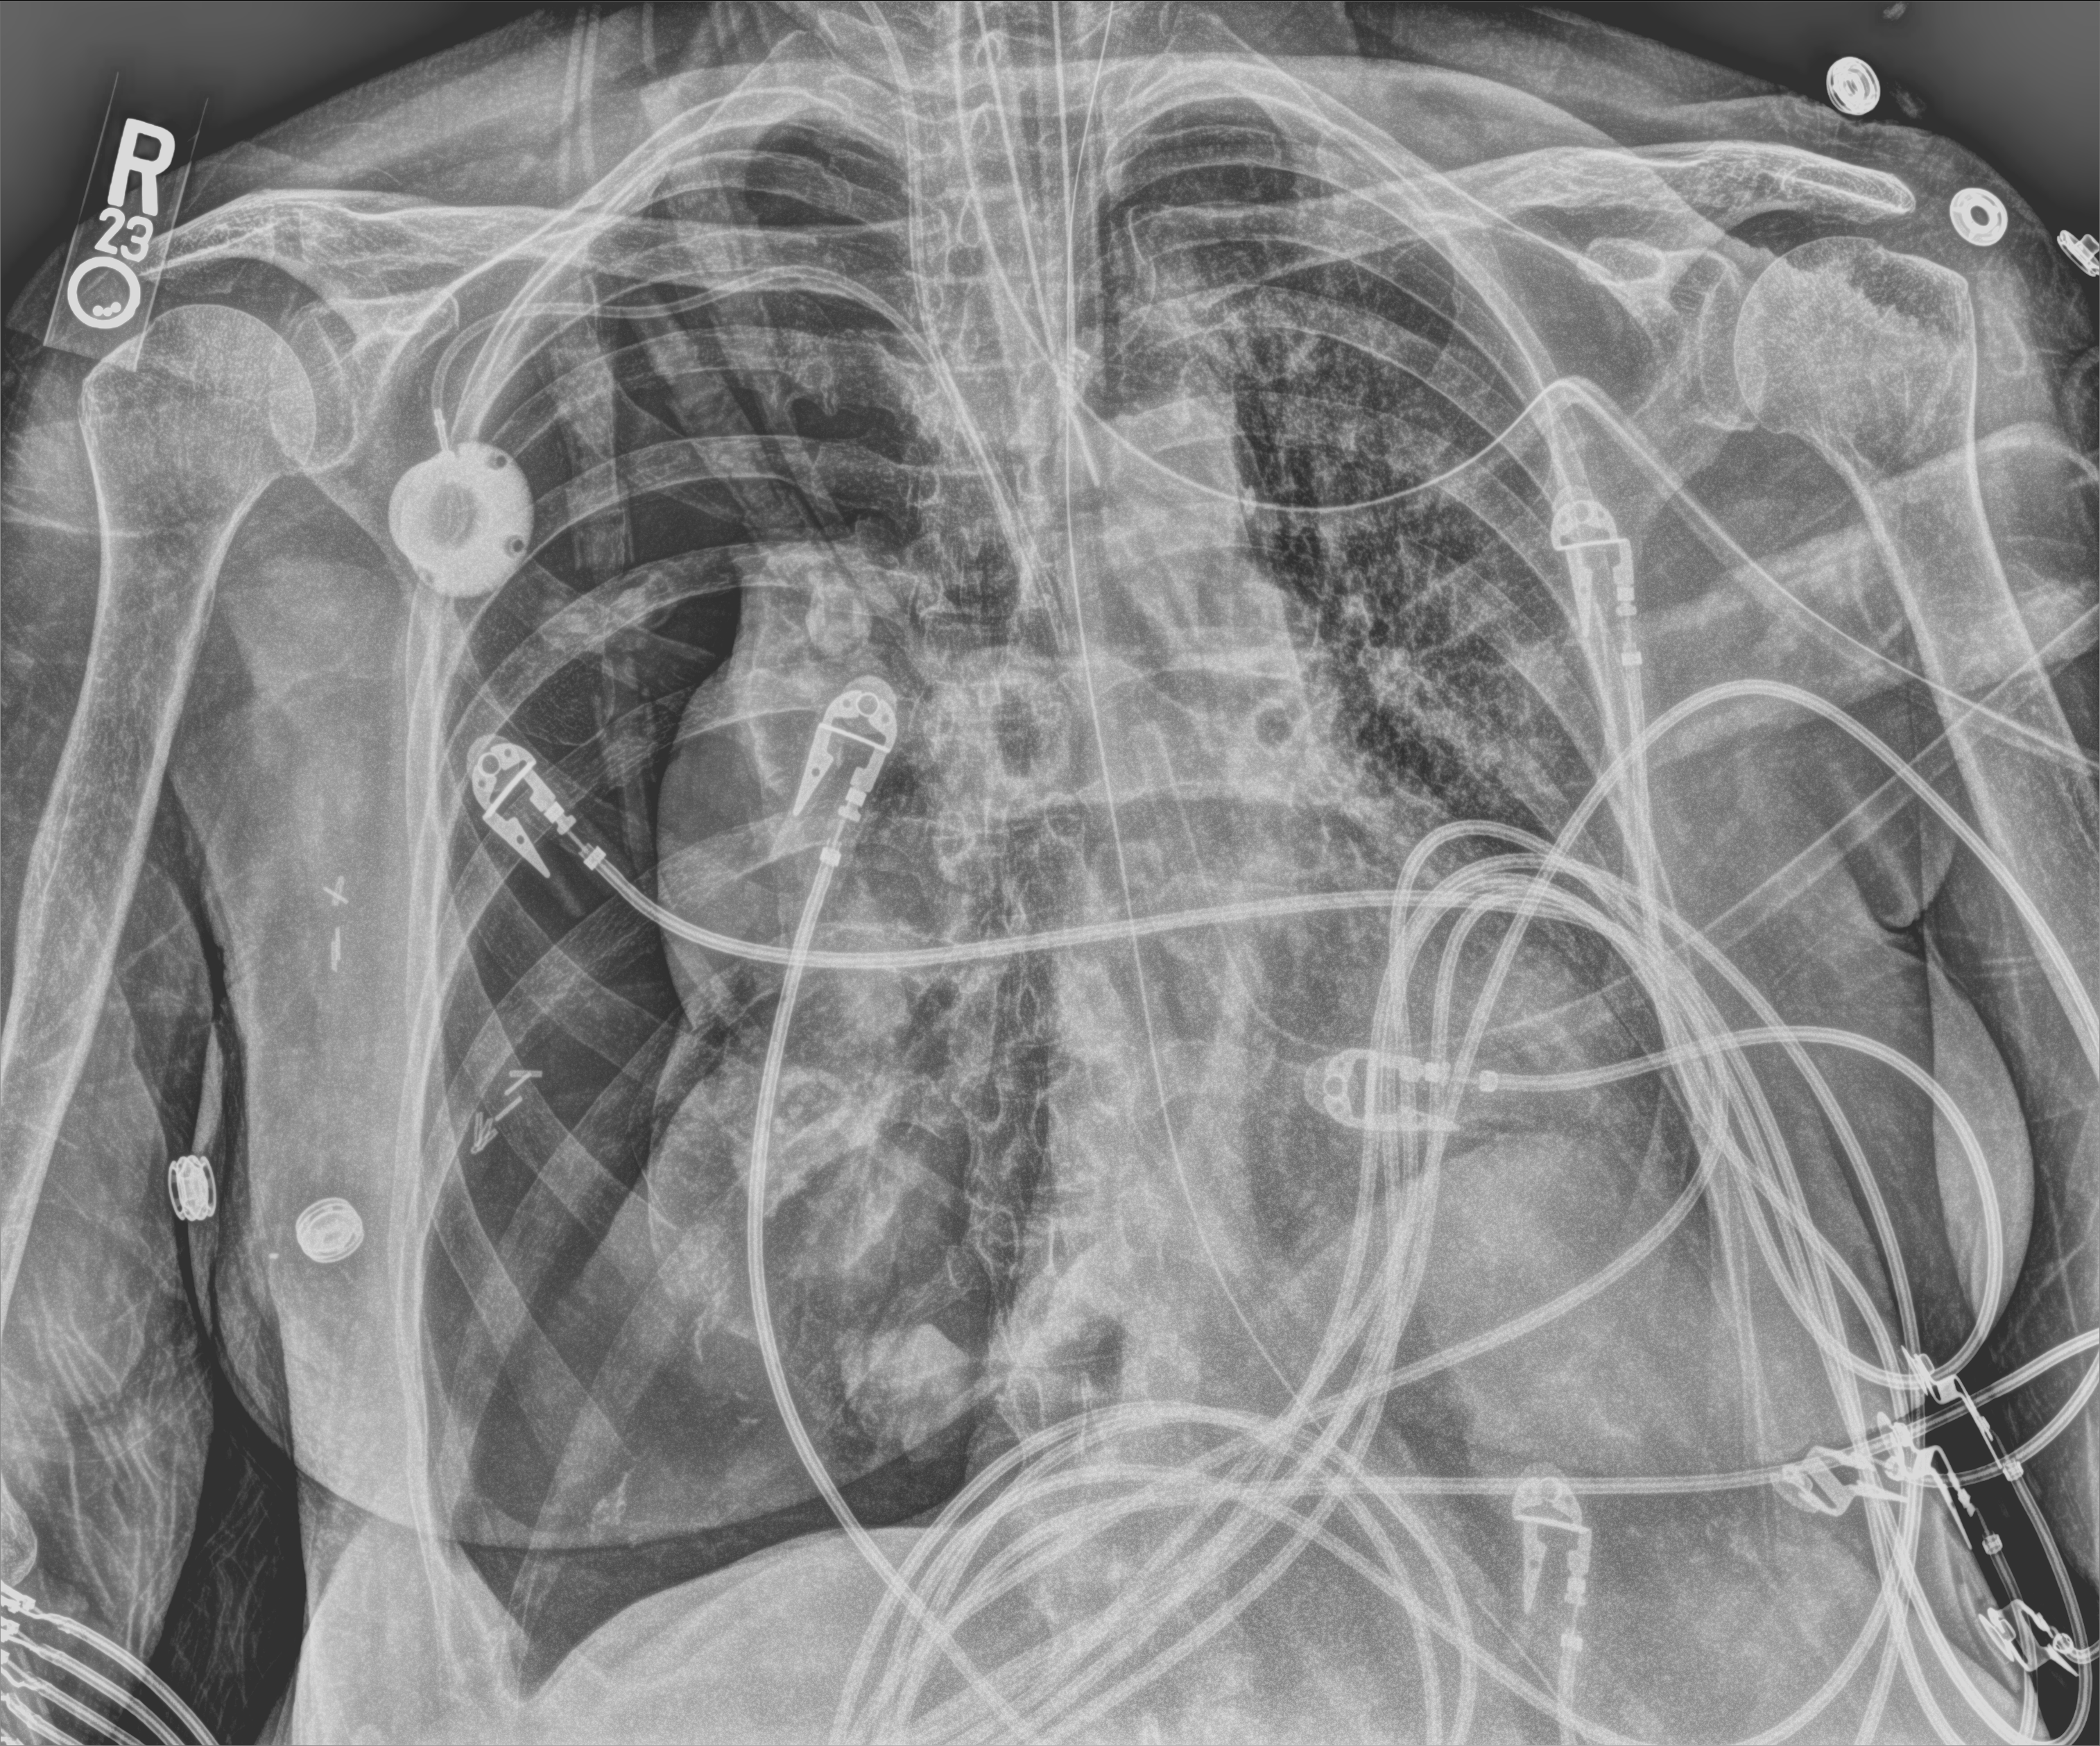
Chest X-ray (portable), anteroposterior (AP) projection. Female patient hospitalised with COVID-19, age 60–74 years.
Hospital-stay facts (about this admission, not read from this image; timing relative to this image not recorded): mechanically ventilated during this hospital stay: yes; length of hospital stay: 43 days; admitted to intensive care during this hospital stay: yes.